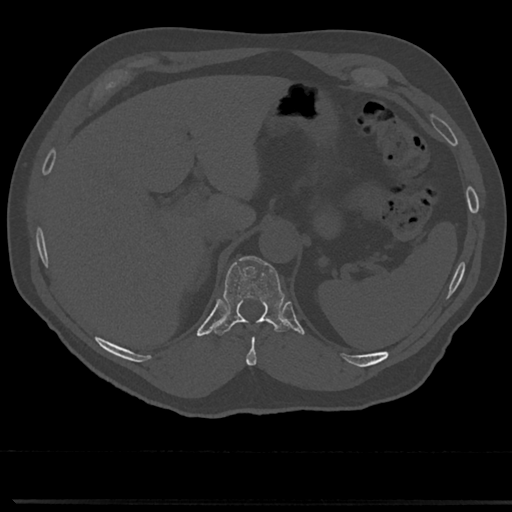
CT including the spine, one axial slice; slice 217 of 817 in the series (ordered by position); reconstruction kernel Br40s/3; bone window (W 1800 / L 400 HU); 0.5 mm slice thickness; 512 × 512 image matrix, field of view 355 × 355 mm. Patient: male, 61 years. From the clinical record (not read from this slice): primary cancer: prostate.
Annotated regions visible in this slice (semi-automatically segmented with operator editing):
- T10 vertebra: bounding box <246,322,270,366> (left, top, right, bottom; pixels)
- T11 vertebra: <217,256,287,335>